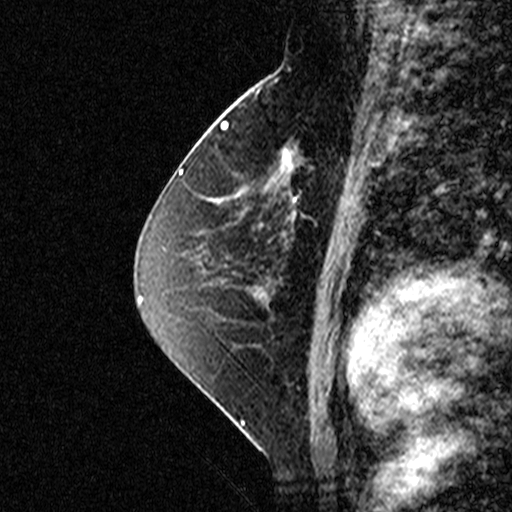
Breast MRI (dynamic contrast-enhanced), one sagittal slice. Slice 22 of 44 in the series (ordered by position). Dynamic contrast-enhanced study with each time point stored as its own series, time point 2 of 3 at this slice position (early post-contrast, ordered by acquisition time). 1.5 T. TE 4.5 ms, TR 11 ms. 3 mm slice thickness. 512 × 512 image matrix, field of view 200 × 200 mm. Female patient, age 49 years. Case-level facts recorded for this patient, not image findings: setting: breast cancer imaged before/during neoadjuvant chemotherapy; receptor status: triple-negative.
Annotated regions visible in this slice (semi-automatically segmented with operator editing):
- analysis volume of interest (the breast-tissue region the enhancement analysis was run in; not a lesion): box from (x=254, y=112) to (x=347, y=207) px
- tumour enhancement mask (voxels above the 90 % enhancement threshold inside the analysis volume of interest): (x=254, y=142)–(x=347, y=202)